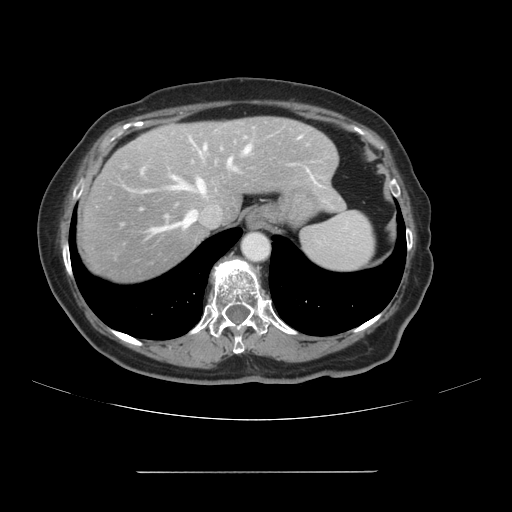
Contrast-enhanced abdominal CT, one axial slice. Slice 85 of 111 in the series (ordered by position). Intravenous contrast given. Soft-tissue window (W 400 / L 40 HU). 2.5 mm slice thickness. 512 × 512 image matrix. Female patient, age 74 years. Case-level facts recorded for this patient, not image findings: diagnosis: colorectal cancer liver metastases, imaged before liver resection; multiple liver metastases: yes; largest metastasis: 1.1 cm.
Structures marked on this image (manually delineated by an expert):
- hepatic veins: box from (x=156, y=139) to (x=298, y=231) px
- liver: (x=76, y=118)–(x=344, y=286)
- planned liver remnant (the part of the liver to remain after resection): (x=165, y=118)–(x=344, y=219)
- portal vein (with intrahepatic branches): (x=198, y=150)–(x=236, y=170)